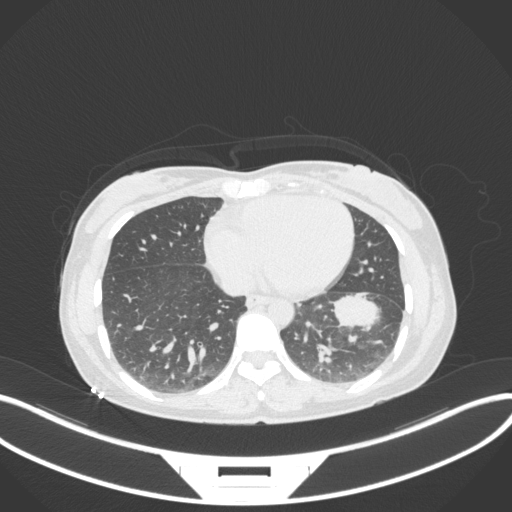
Chest CT, one axial slice; slice 127 of 361 in the series (ordered by position); reconstruction kernel B31f; 120 kVp; lung window (W 1500 / L -600 HU); 1 mm slice thickness; 512 × 512 image matrix. Female patient, age 41 years. From the clinical record (not read from this slice): clinical TNM (as recorded): T2a N3 M1b.
Structures marked on this image (rectangle marked by the reading radiologist):
- lung tumour (recorded histology: adenocarcinoma): bounding box [x1, y1, x2, y2] px = [329, 286, 389, 336]